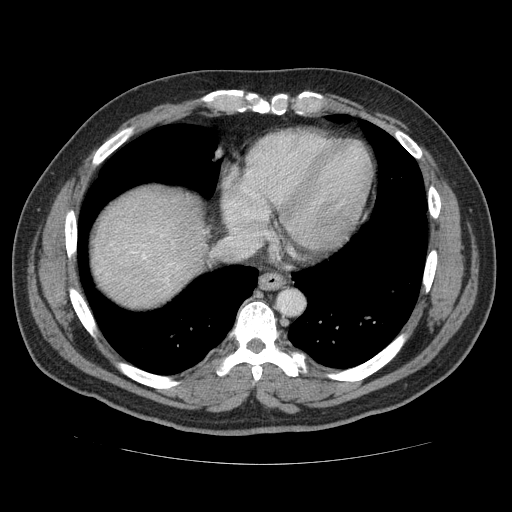
Contrast-enhanced abdominal CT (liver protocol), one axial slice; slice 108 of 113 in the series (ordered by position); reconstruction kernel STANDARD; 120 kVp; soft-tissue window (W 400 / L 40 HU); 512 × 512 image matrix. From the clinical record (not read from this slice): diagnosis: hepatocellular carcinoma (patient treated with transarterial chemoembolisation; whether this scan precedes or follows treatment is not stated here); TNM stage (as recorded): Stage-II; Child-Pugh class: B; tumour differentiation: moderately differentiated; tumour size: 4.8 cm.
Structures marked on this image (semi-automatically segmented with operator editing):
- abdominal aorta: bounding box (x1, y1, x2, y2) in pixels: (279, 291, 302, 315)
- liver parenchyma outside the tumour (the mass and vessels are separate outlines, so this box may not span the whole liver): (94, 188, 202, 300)